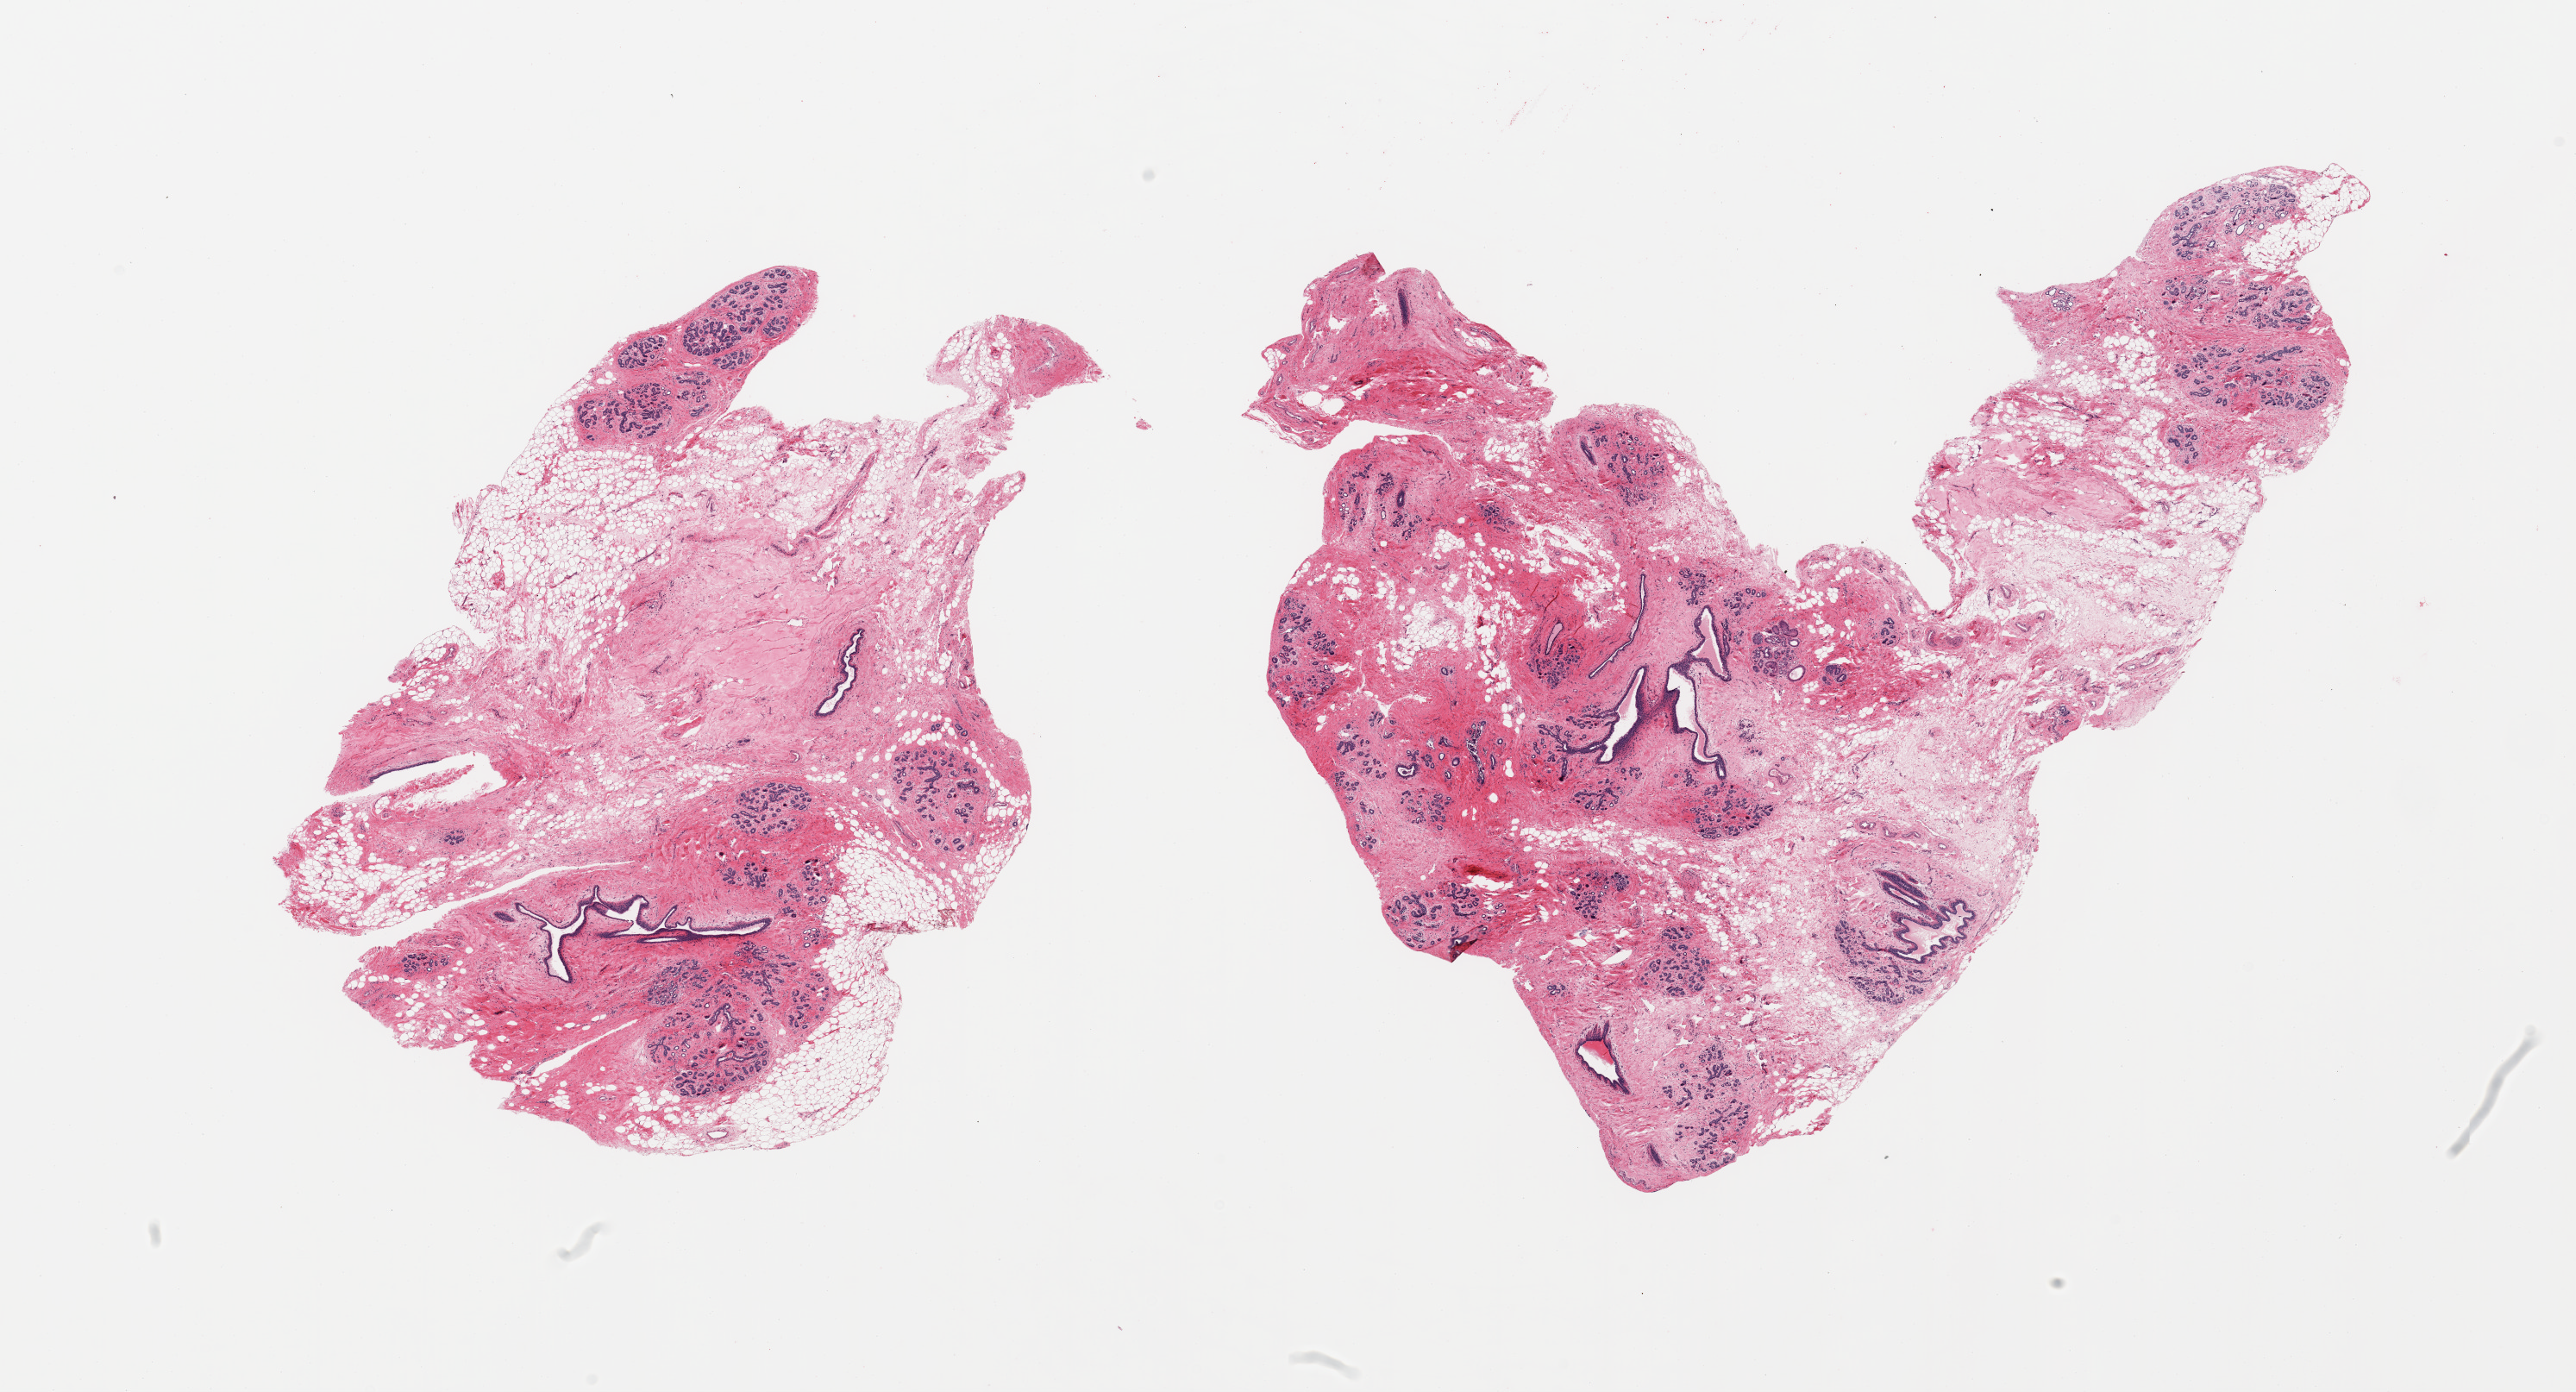
Digitized H&E-stained section — low-resolution overview of the scanned area, about 23.6 x 12.8 mm; PAXgene-fixed, paraffin-embedded tissue; sampled site (target tissue): breast; tissue donor sample. Donor: female.
Reviewer comment on this tissue sample: 2 pieces; mature adipose tissue and lobular and ductal structures embedded in fibrotic stroma with focal area of periductal hyalinization.